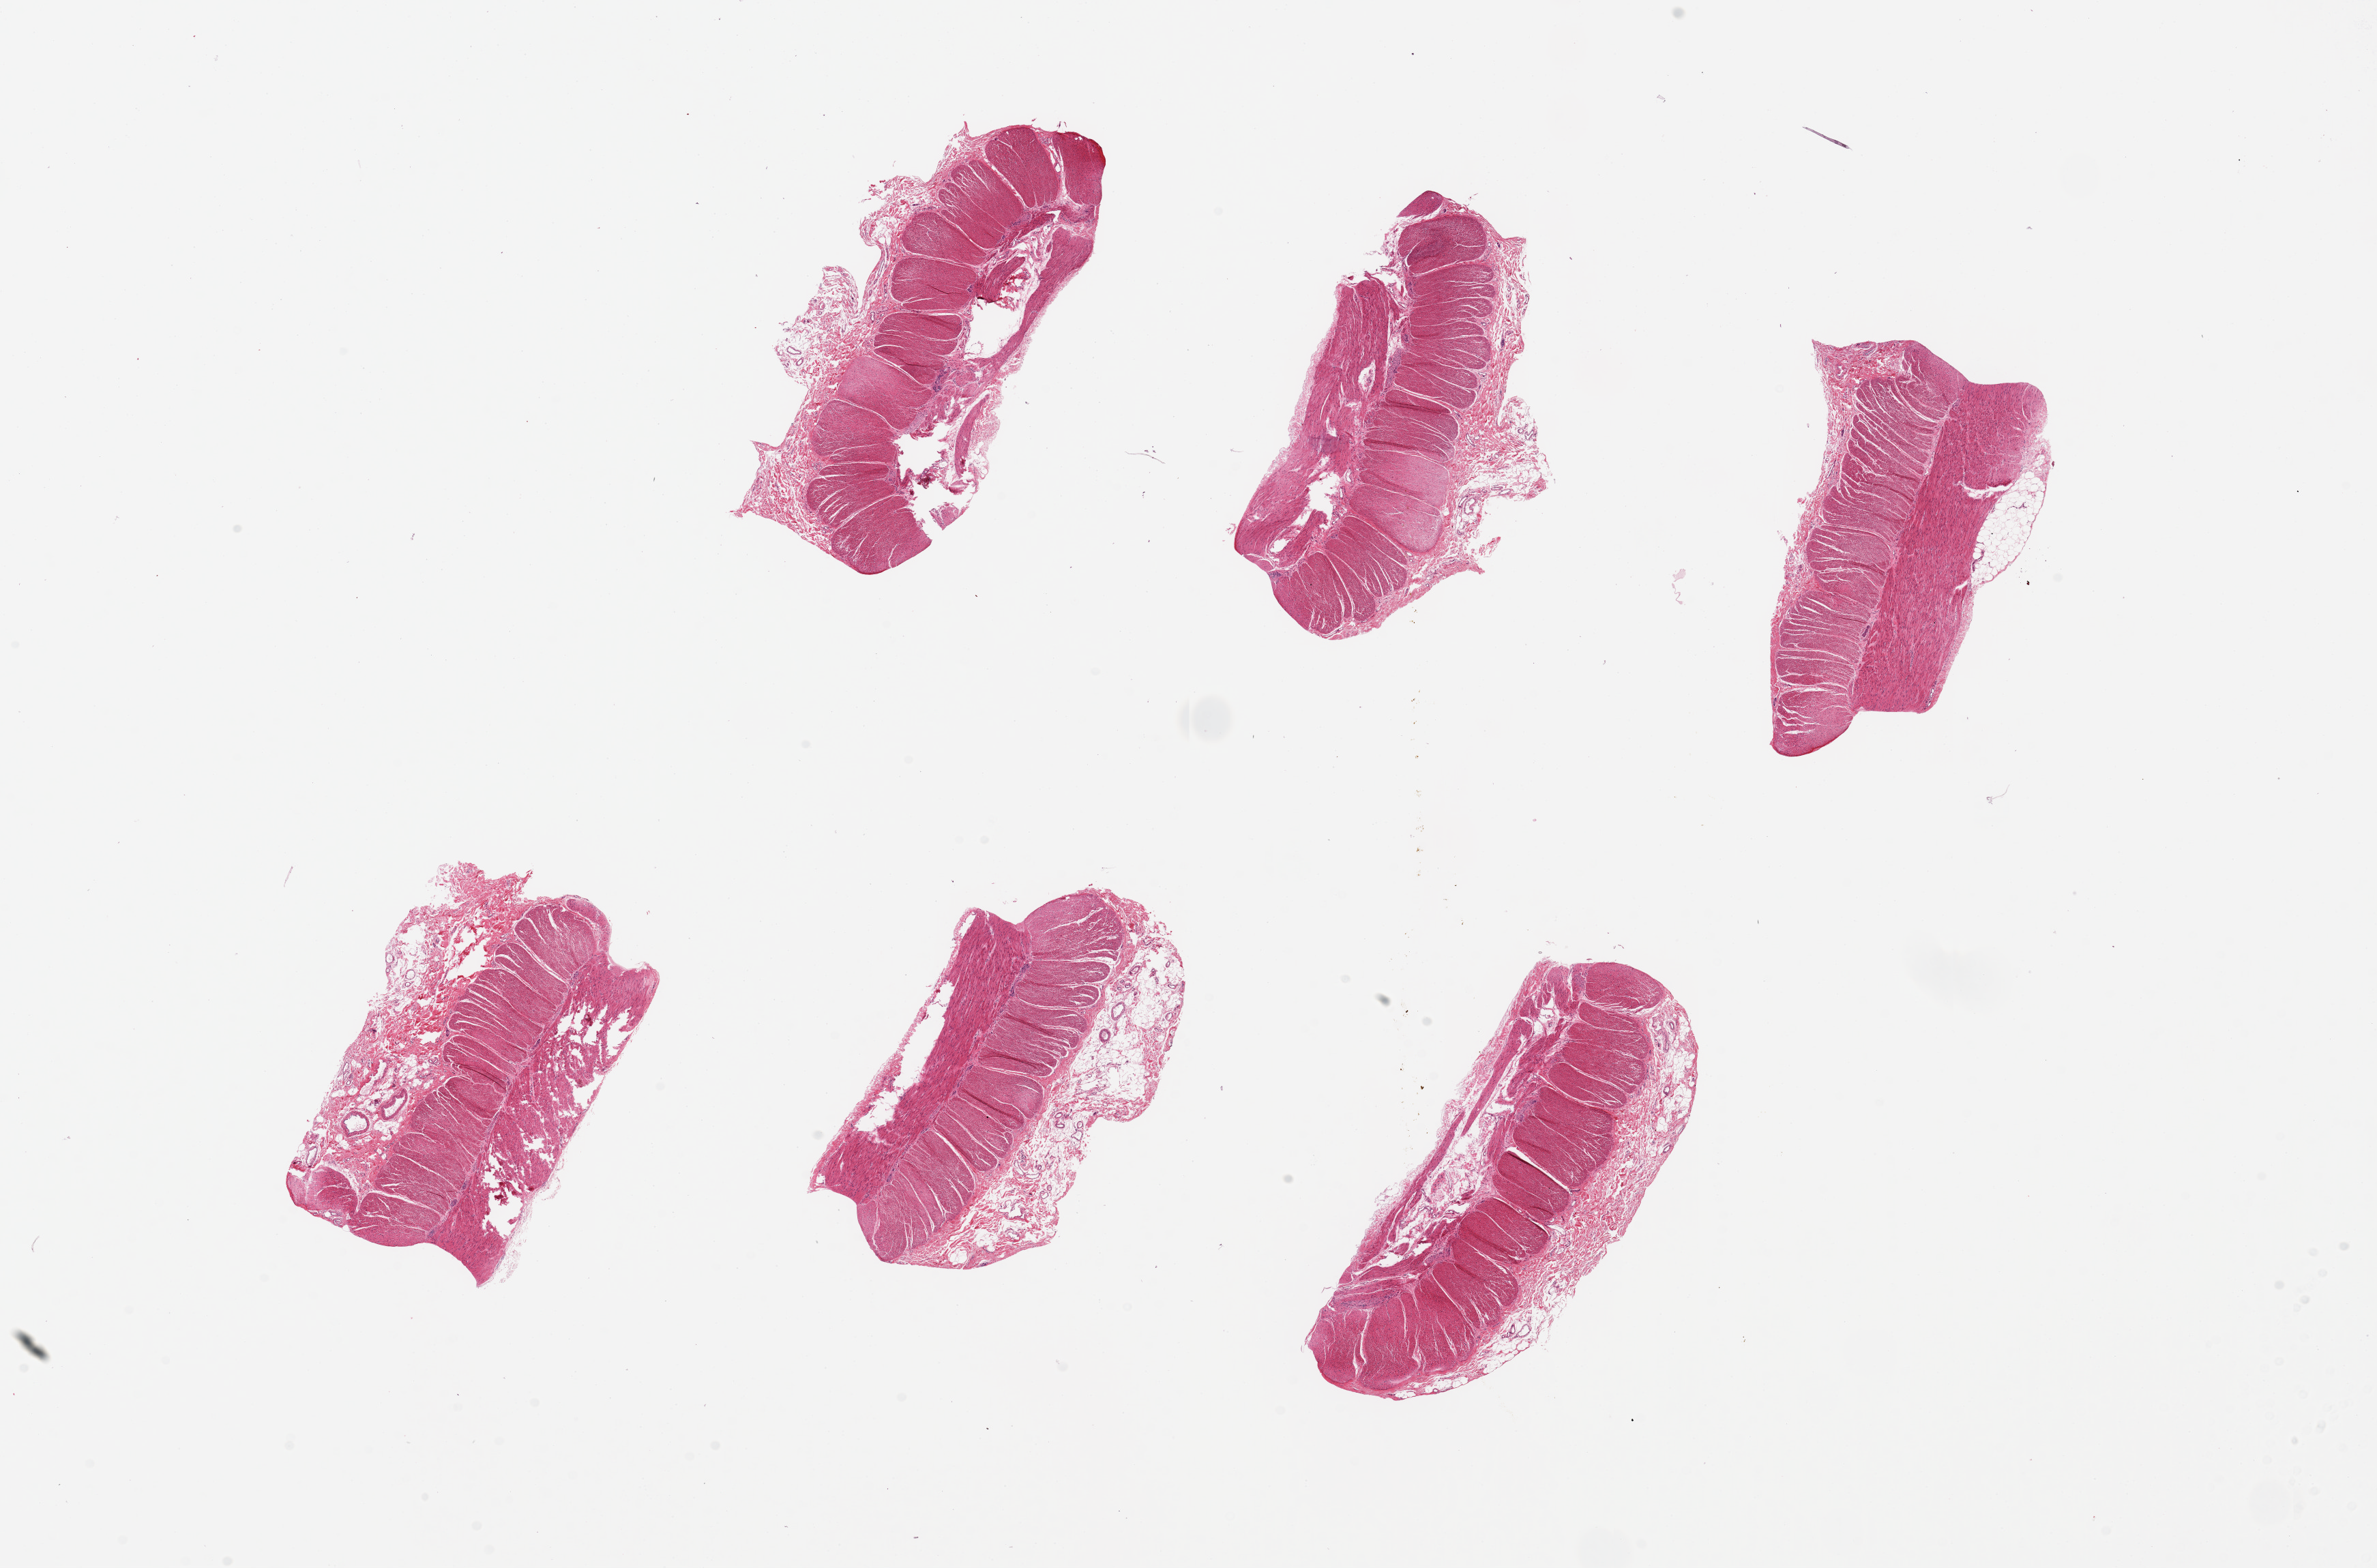
Whole-slide image, haematoxylin and eosin stain — whole scanned area (about 27.6 x 18.2 mm, acquisition: 20x scan) shown as a low-resolution overview; PAXgene-fixed, paraffin-embedded tissue; section of sigmoid colon (target tissue); donor tissue sample.
Review note (as recorded): 6 pieces, up to 6x2.5mm; Well-sampled muscularis (without mucosa); good ganglion cells.